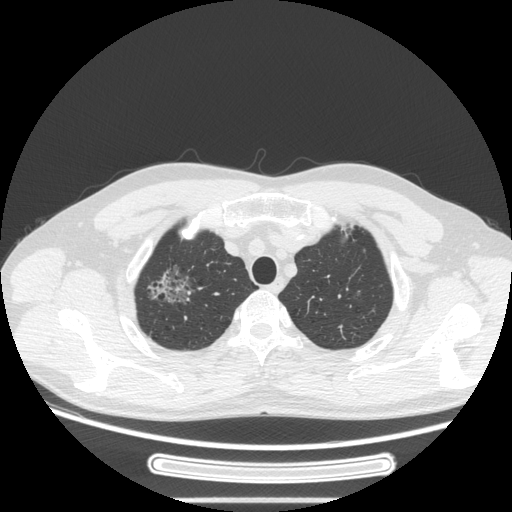
Chest CT, one axial slice. Position 225 of 269 along the scan axis. Reconstruction kernel STANDARD. Lung window (W 1500 / L -600 HU). 1.25 mm slice thickness. 512 × 512 image matrix. Male patient, age 53 years. Case-level facts recorded for this patient, not image findings: clinical TNM (as recorded): T1c N0 M0; histopathological grade: G2.
Structures marked on this image (rectangle marked by the reading radiologist):
- lung tumour (recorded histology: adenocarcinoma): bounding box [x1, y1, x2, y2] px = [144, 256, 192, 312]